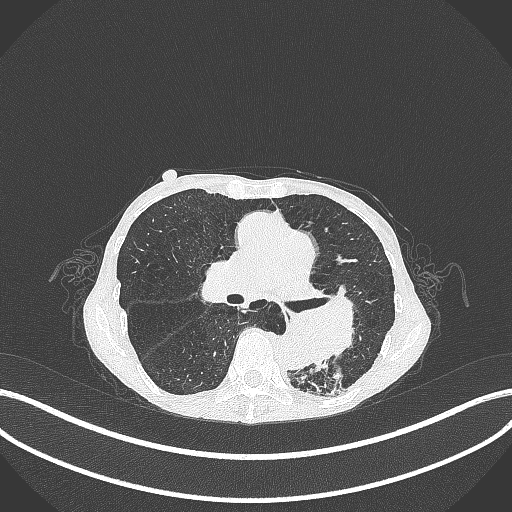
Chest CT, one axial slice. Slice 155 of 347 in the series (ordered by position). Reconstruction kernel B70f. 120 kVp. Lung window (W 1500 / L -600 HU). 1 mm slice thickness. 512 × 512 image matrix, field of view 400 × 400 mm. Female patient, age 70 years. Case-level facts recorded for this patient, not image findings: clinical TNM (as recorded): T3 N0 M0; histopathological grade: G3.
Outlined on this slice (rectangle marked by the reading radiologist):
- lung tumour (recorded histology: small cell carcinoma): bounding box [x1, y1, x2, y2] px = [270, 295, 364, 376]